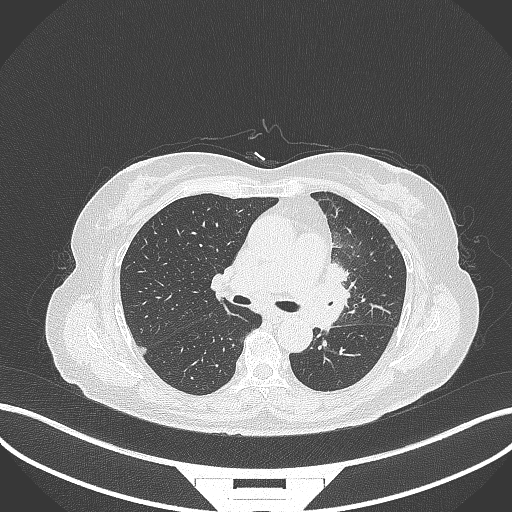
Chest CT, one axial slice; slice 200 of 382 in the series (ordered by position); reconstruction kernel B70f; lung window (W 1500 / L -600 HU); 1 mm slice thickness; 512 × 512 image matrix, field of view 400 × 400 mm. Patient: female, 64 years. From the clinical record (not read from this slice): clinical TNM (as recorded): T2a N2 M0.
Structures marked on this image (bounding box drawn by a radiologist):
- lung tumour (recorded histology: adenocarcinoma): box from (x=322, y=256) to (x=361, y=332) px